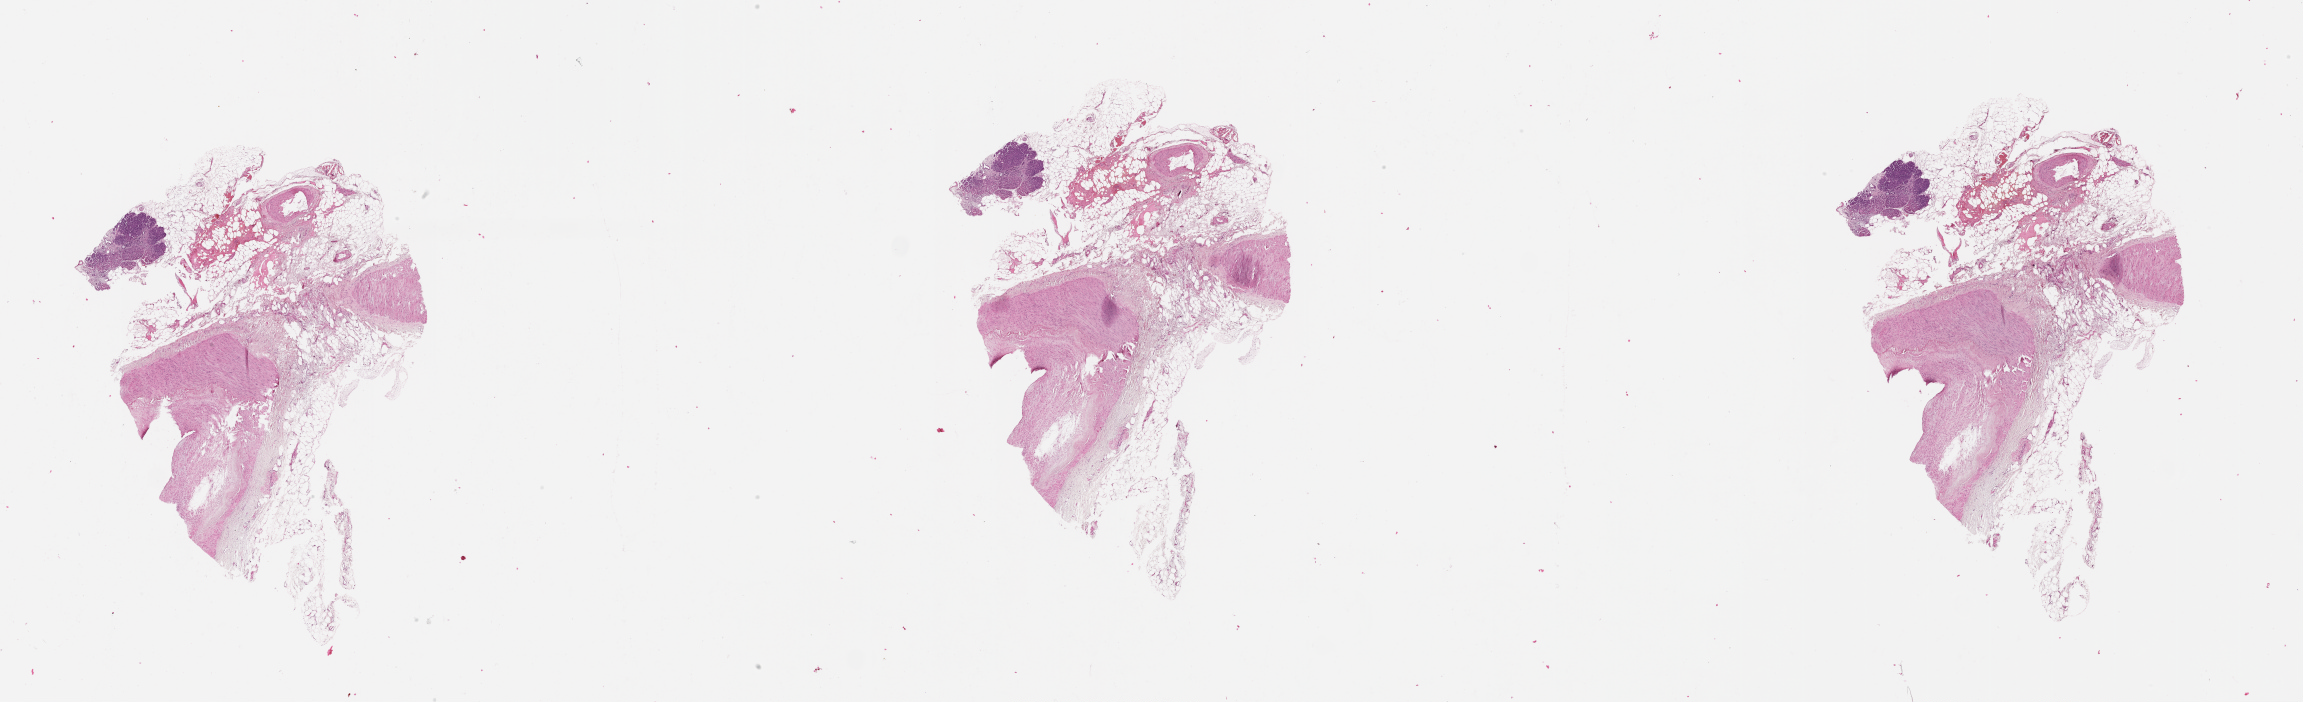
Digitized Hematoxylin and eosin (H&E) stained tissue section (whole slide), low-resolution overview of the scanned area, about 37.1 x 11.3 mm. Normal (non-tumour) tissue sample, pancreas. Male, 77 y/o.
- this section: normal (non-tumour) tissue from the same patient
- patient diagnosis (cohort enrolment): ductal adenocarcinoma (pancreas)